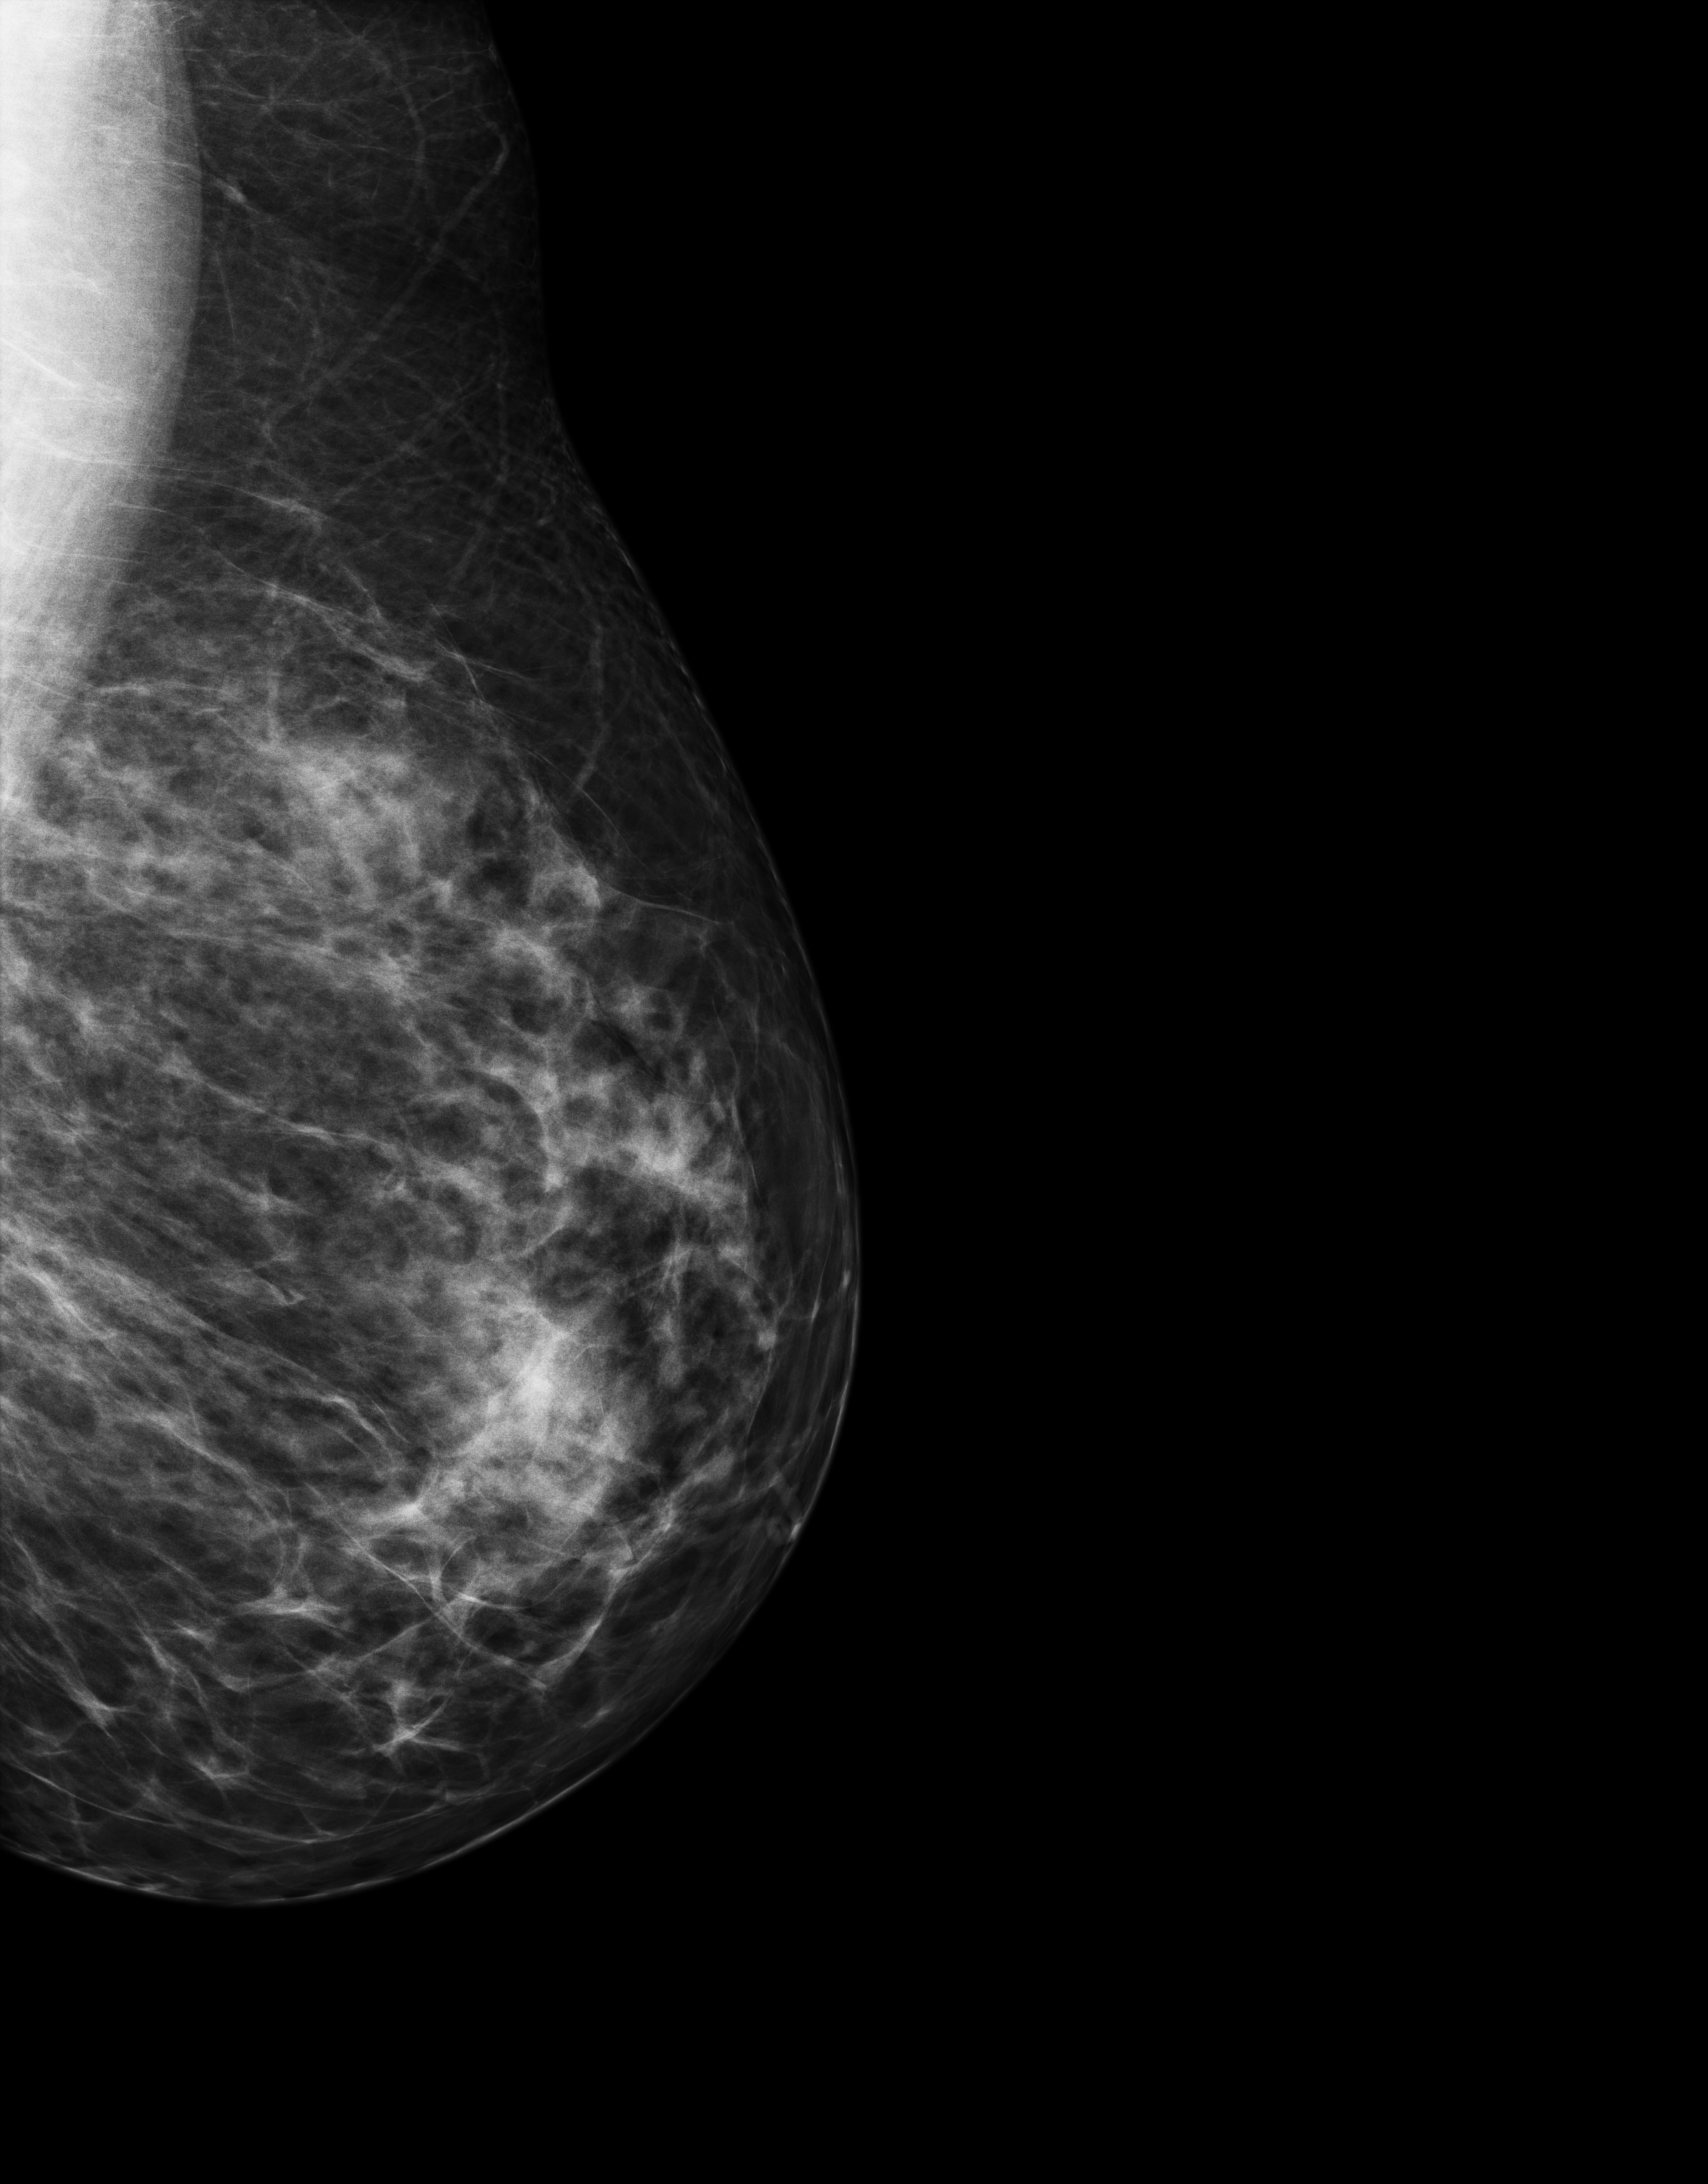
Full-field digital mammogram (FFDM); left breast; laterally exaggerated craniocaudal (XCCL) view; annual screening mammography examination; compressed breast thickness 95 mm. Female patient, age 42 years.
- breast density at the screening exam (both breasts): heterogeneously dense (BI-RADS density category c)
- final BI-RADS category for the screening round (tomosynthesis exam, both breasts): category 1
- recall: no recall after this screen